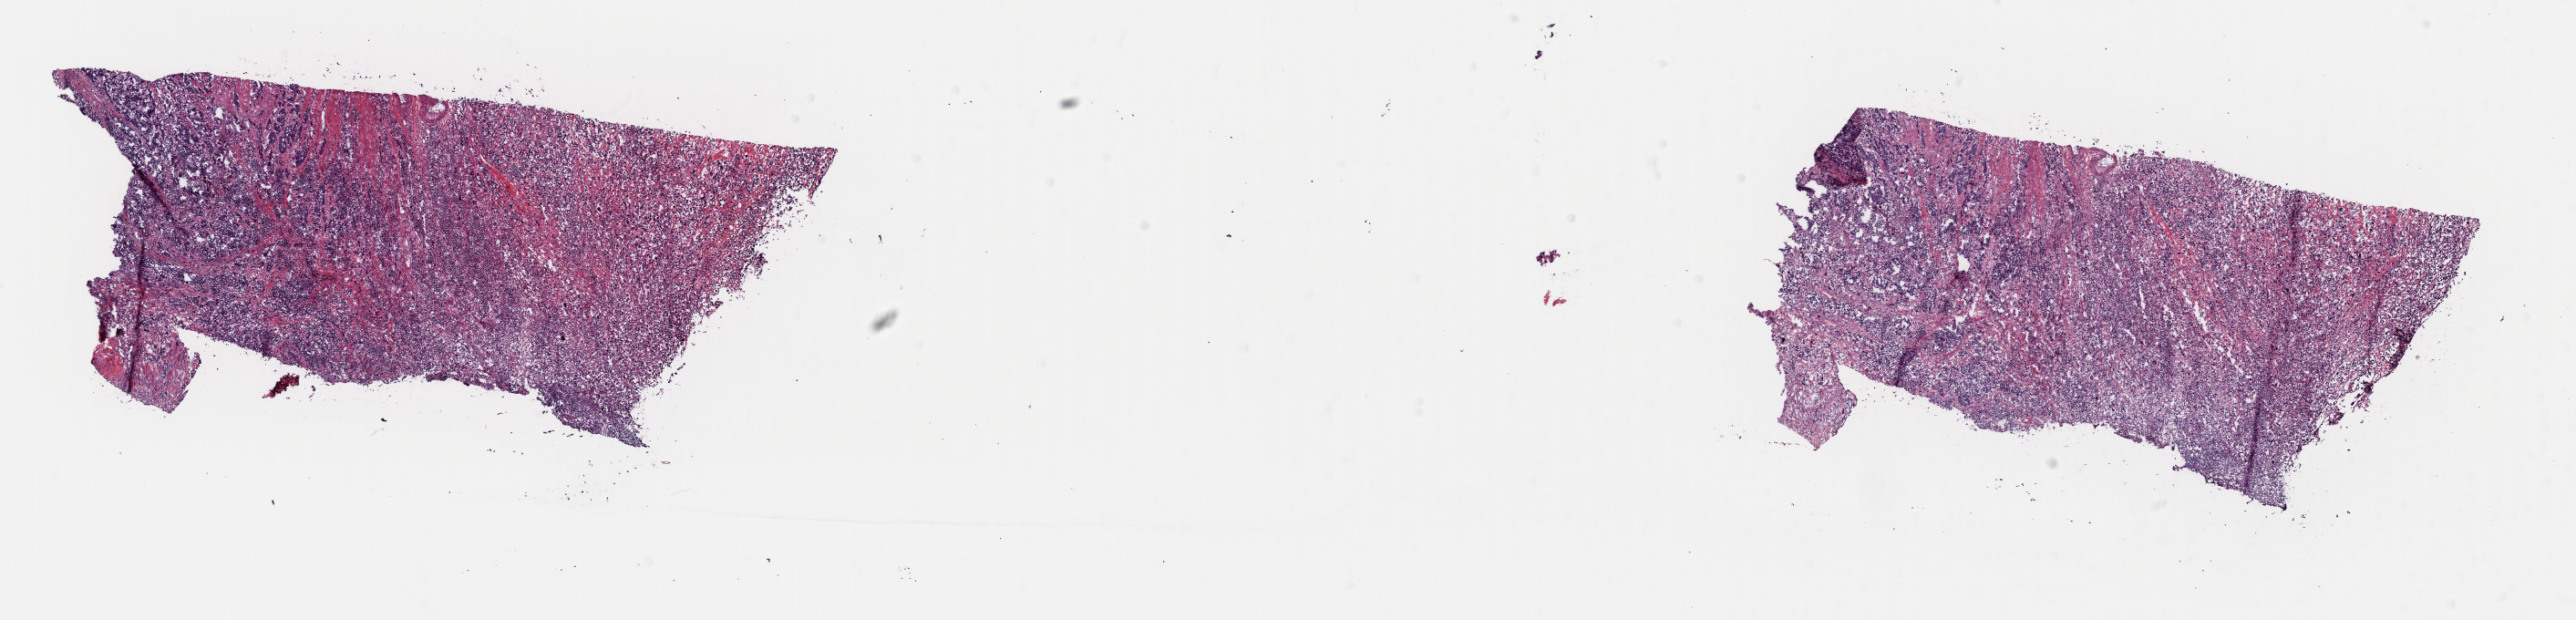
Hematoxylin and eosin (H&E) stained whole-slide image — whole scanned area (about 22.3 x 5.4 mm, acquisition: 40x scan) shown as a low-resolution overview, frozen section from the top of the tissue portion, primary tumour sample from the bladder. Male patient; age at initial diagnosis 76 years. Histologic grade: high grade. Composition of this section per pathologist review: tumour cells 75%, tumour nuclei 75%, normal cells 0%, stromal cells 25%, necrosis 0%. Infiltration values recorded for this section: lymphocyte infiltration 5%, monocyte infiltration 0%, neutrophil infiltration 0%.
AJCC pathologic stage: IV (7th edition). Lymph nodes positive (case pathology): 34 of 34 examined. Pathologic diagnosis: Transitional cell carcinoma (trigone of bladder).